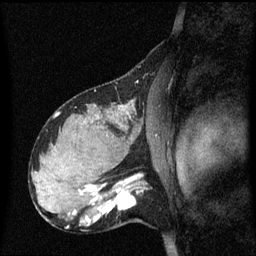
Breast MRI (dynamic contrast-enhanced), one sagittal slice; dynamic contrast-enhanced series, image 2 of 3 at this slice position (ordered by acquisition); 1.5 T; TE 4.2 ms, TR 8.4 ms; 2.1 mm slice thickness; 256 × 256 image matrix, field of view 210 × 210 mm. Patient: female, 31 years. From the clinical record (not read from this slice): setting: breast cancer imaged before/during neoadjuvant chemotherapy; receptor status: HR-positive, HER2-negative.
Outlined on this slice (semi-automatically segmented with operator editing):
- analysis volume of interest (the breast-tissue region the enhancement analysis was run in; not a lesion): bounding box [x1, y1, x2, y2] px = [98, 175, 151, 227]
- tumour enhancement mask (voxels above the 70 % enhancement threshold inside the analysis volume of interest): [99, 177, 139, 213]